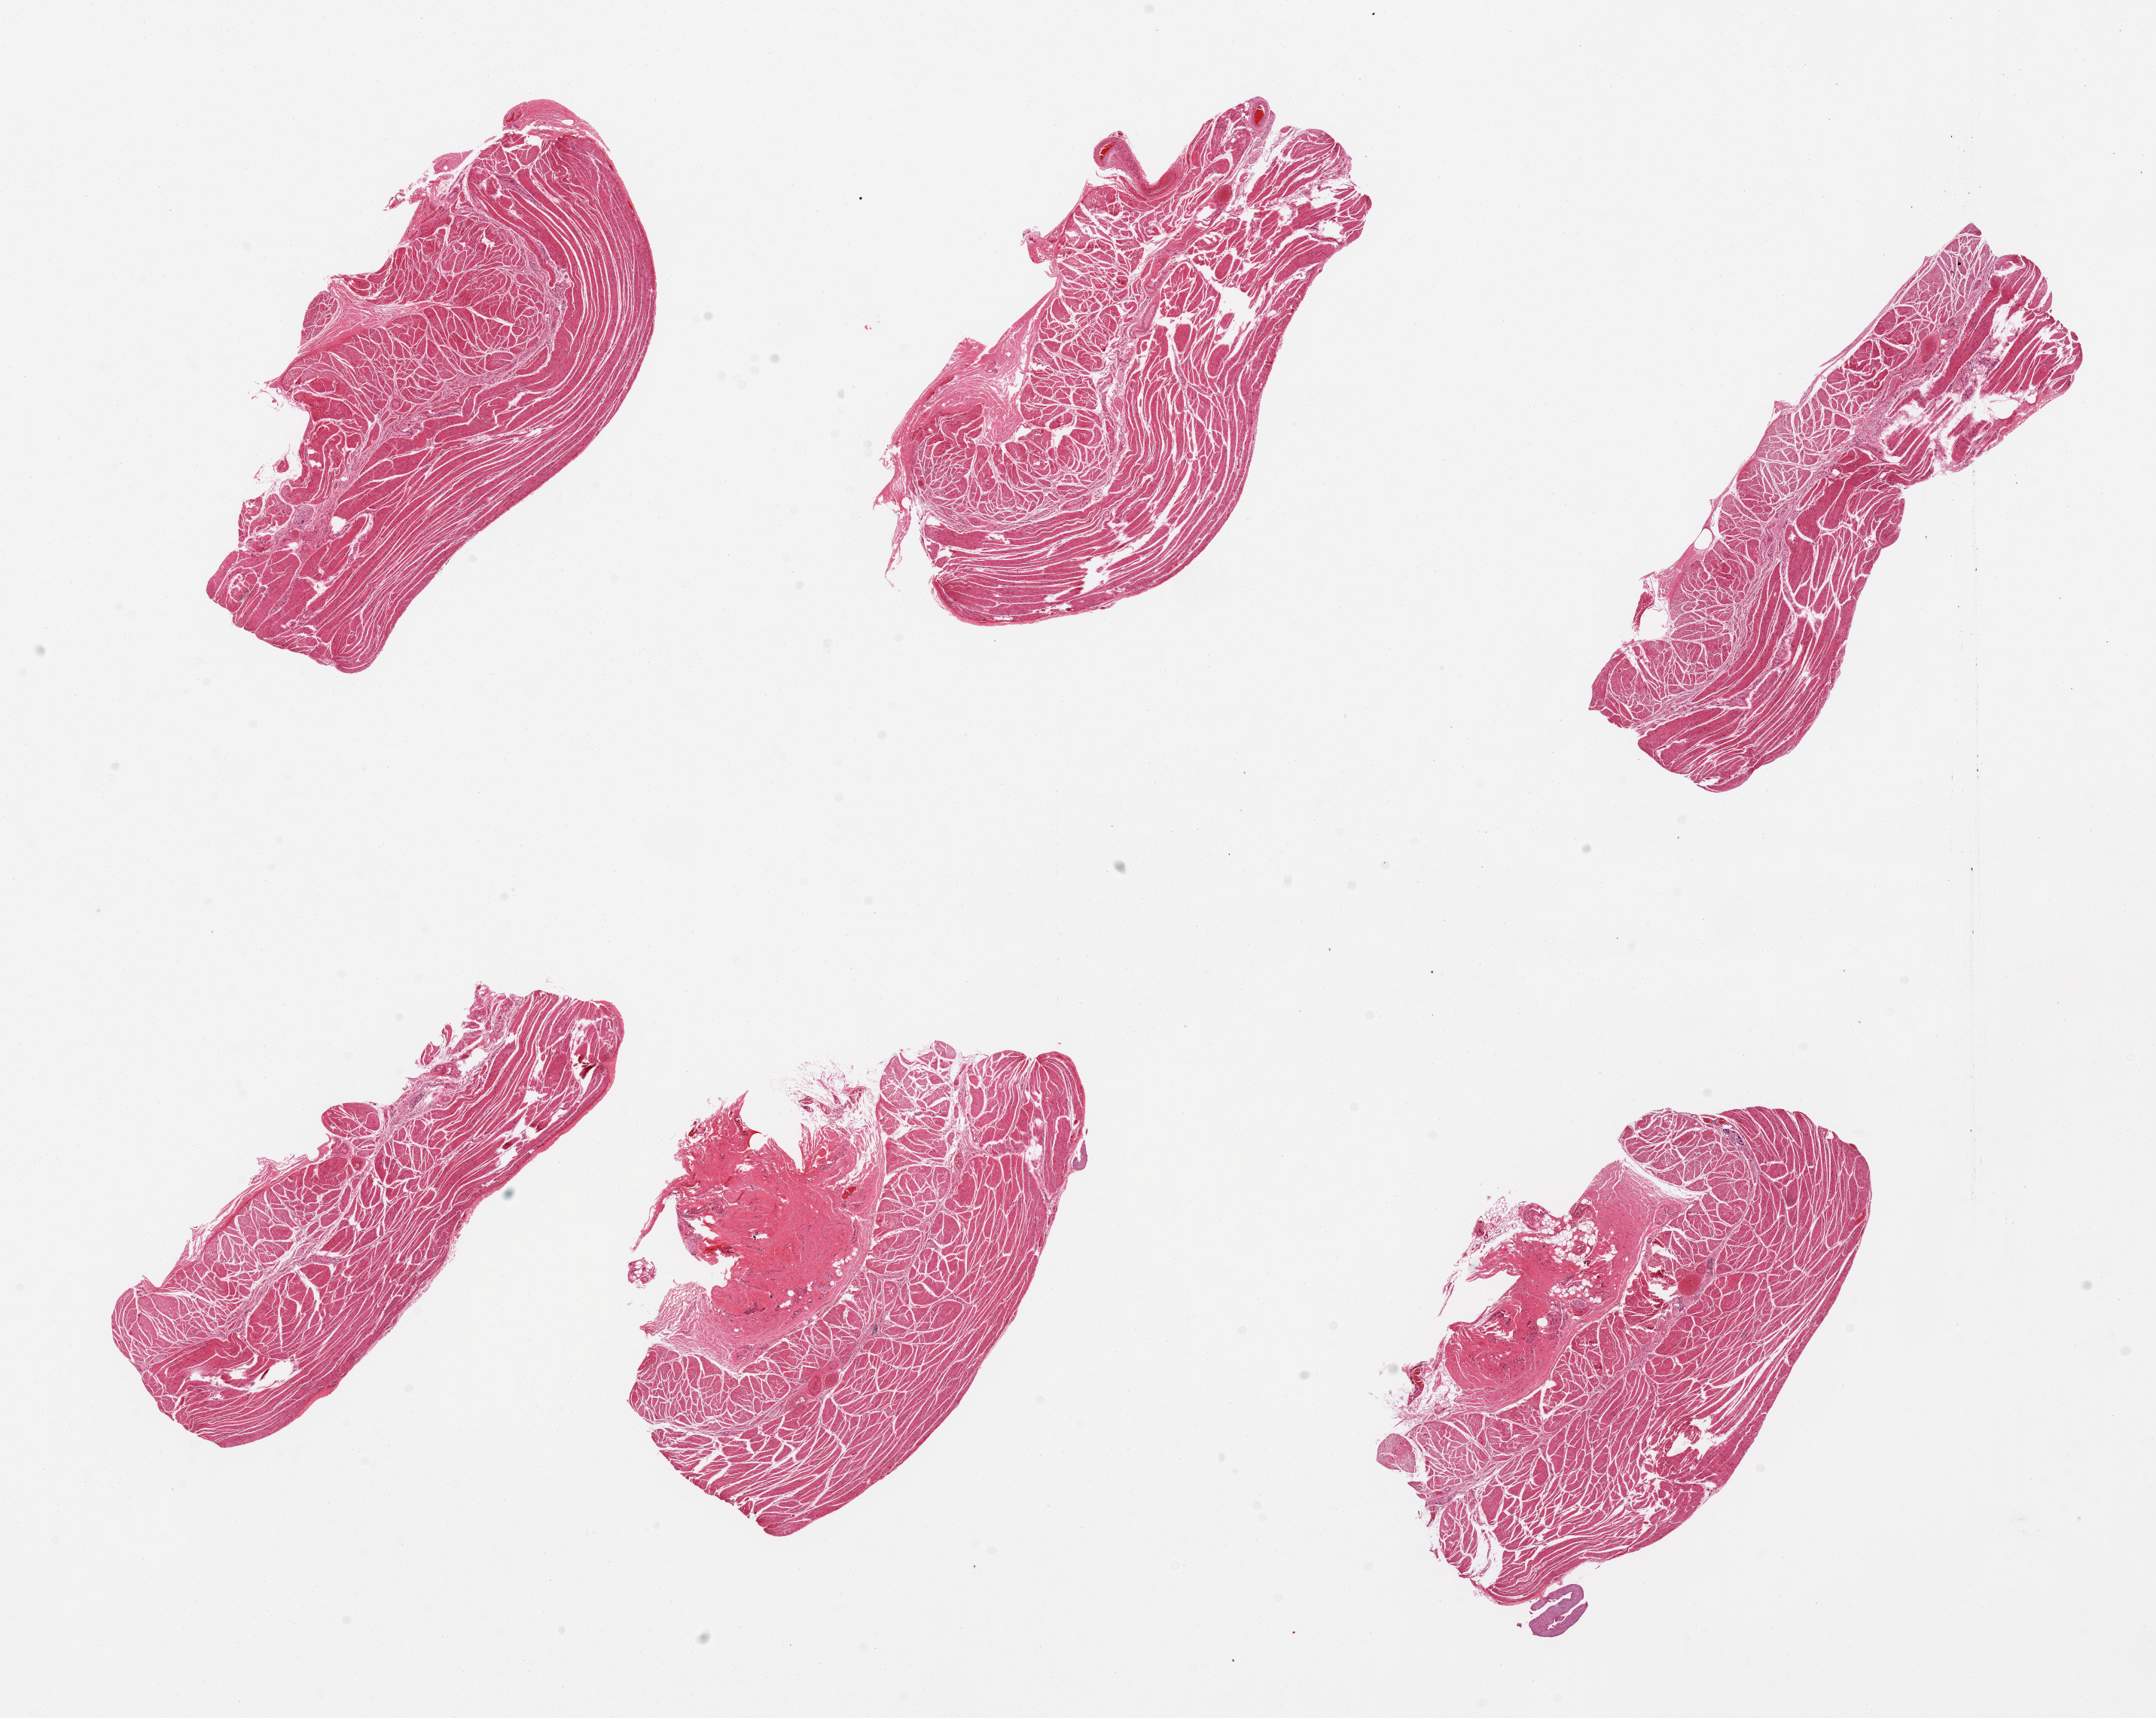
Digitized haematoxylin and eosin-stained section, shown as a low-resolution overview of the whole scanned area (about 22.6 x 18.0 mm). PAXgene-fixed paraffin-embedded (PFPE) section. Section of esophageal muscle (target tissue). Donor tissue sample. Donor sex: male.
Pathologist's review note for this sample: 6 pieces; prominent (30 & 20%) submucosal fibrous tissue in 2 of 6 pieces.